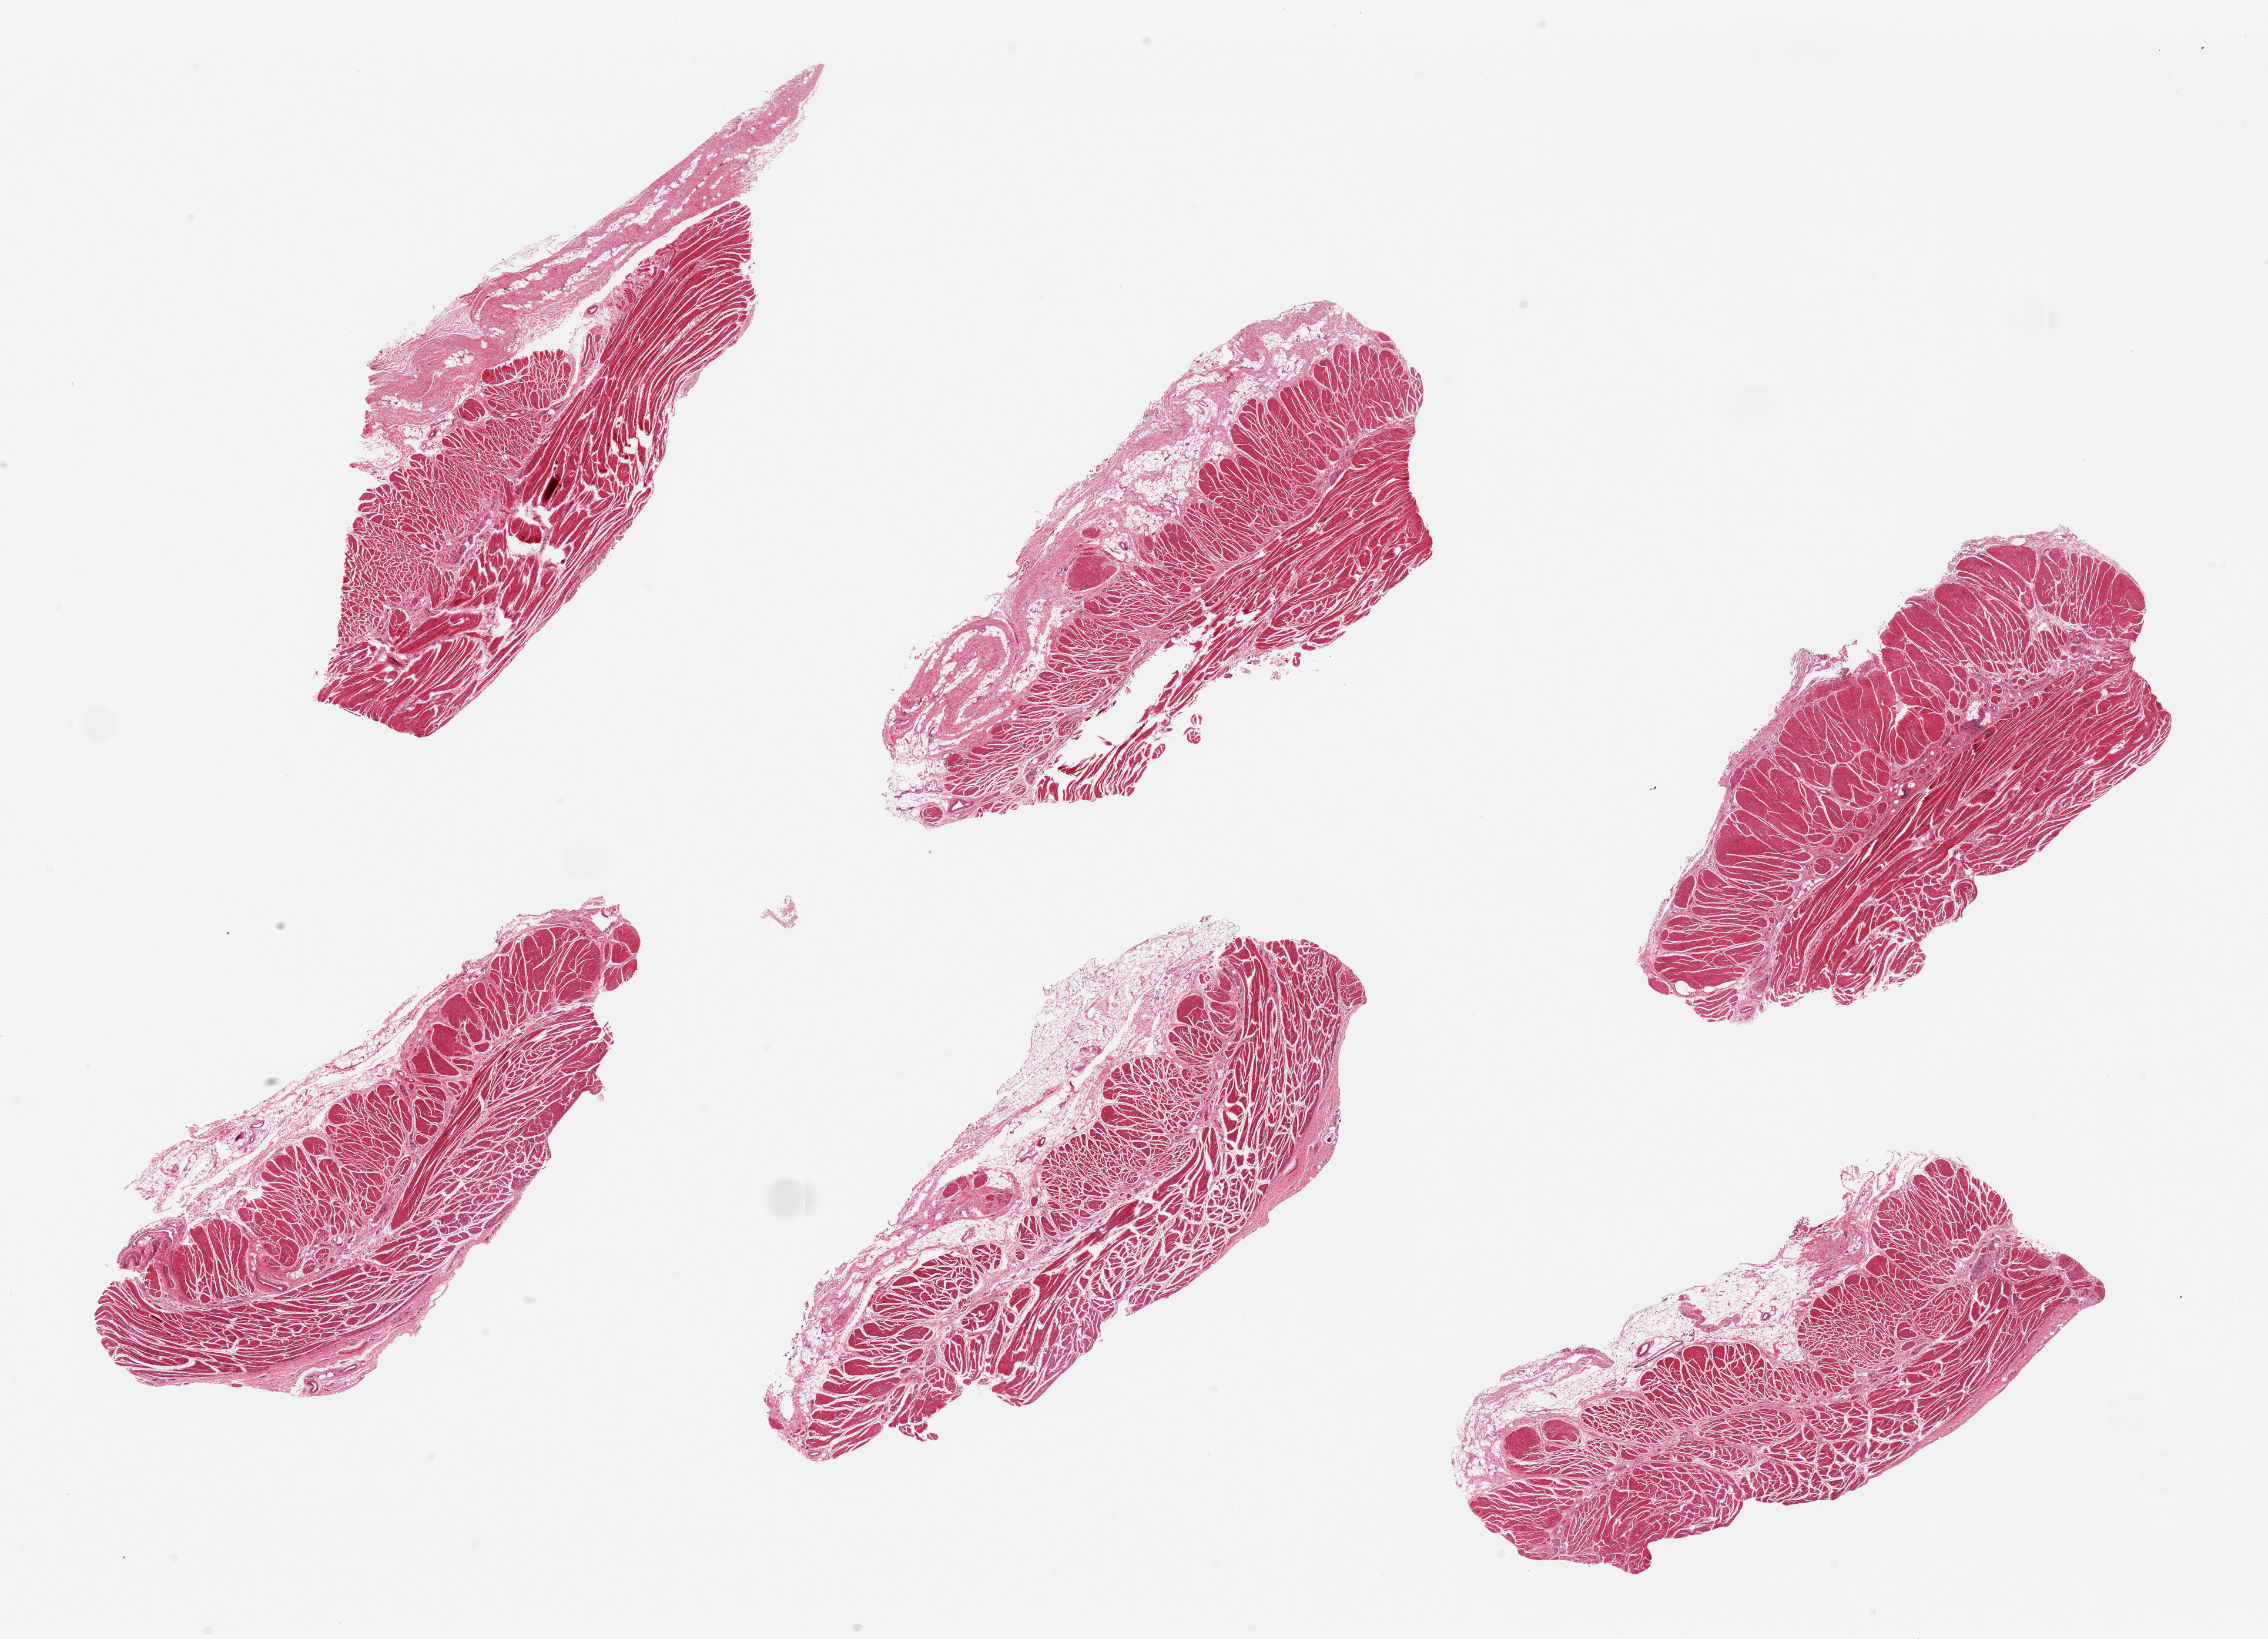
Digitized H&E-stained section, brightfield, shown as a low-resolution overview of the whole scanned area (about 30.5 x 22.0 mm). PAXgene-fixed, paraffin-embedded tissue. Section of gastroesophageal junction (target tissue). Donor tissue sample.
Reviewer comment on this tissue sample: 6 pieces; smooth muscle layers with adherent serosal fat on 5 of 6 pieces, up to 1.3 mm thick.